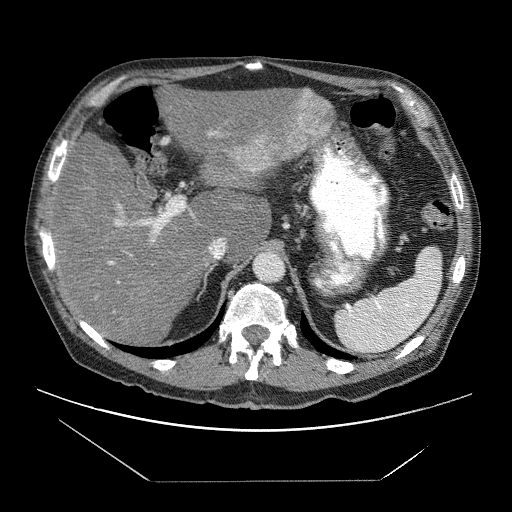
Contrast-enhanced abdominal CT (liver protocol), one axial slice. Slice 43 of 83 in the series (ordered by position). Reconstruction kernel STANDARD. Soft-tissue window (W 400 / L 40 HU). 2.5 mm slice thickness. 512 × 512 image matrix, field of view 420 × 420 mm. From the clinical record (not read from this slice): diagnosis: hepatocellular carcinoma (patient treated with transarterial chemoembolisation; whether this scan precedes or follows treatment is not stated here); TNM stage (as recorded): Stage-IVB.
Outlined on this slice (semi-automatic segmentation, software-assisted and operator-edited):
- liver parenchyma outside the tumour (the mass and vessels are separate outlines, so this box may not span the whole liver): bounding box (x1, y1, x2, y2) in pixels: (48, 76, 332, 338)
- mass: (235, 89, 334, 175)
- liver vessels: (54, 131, 218, 284)